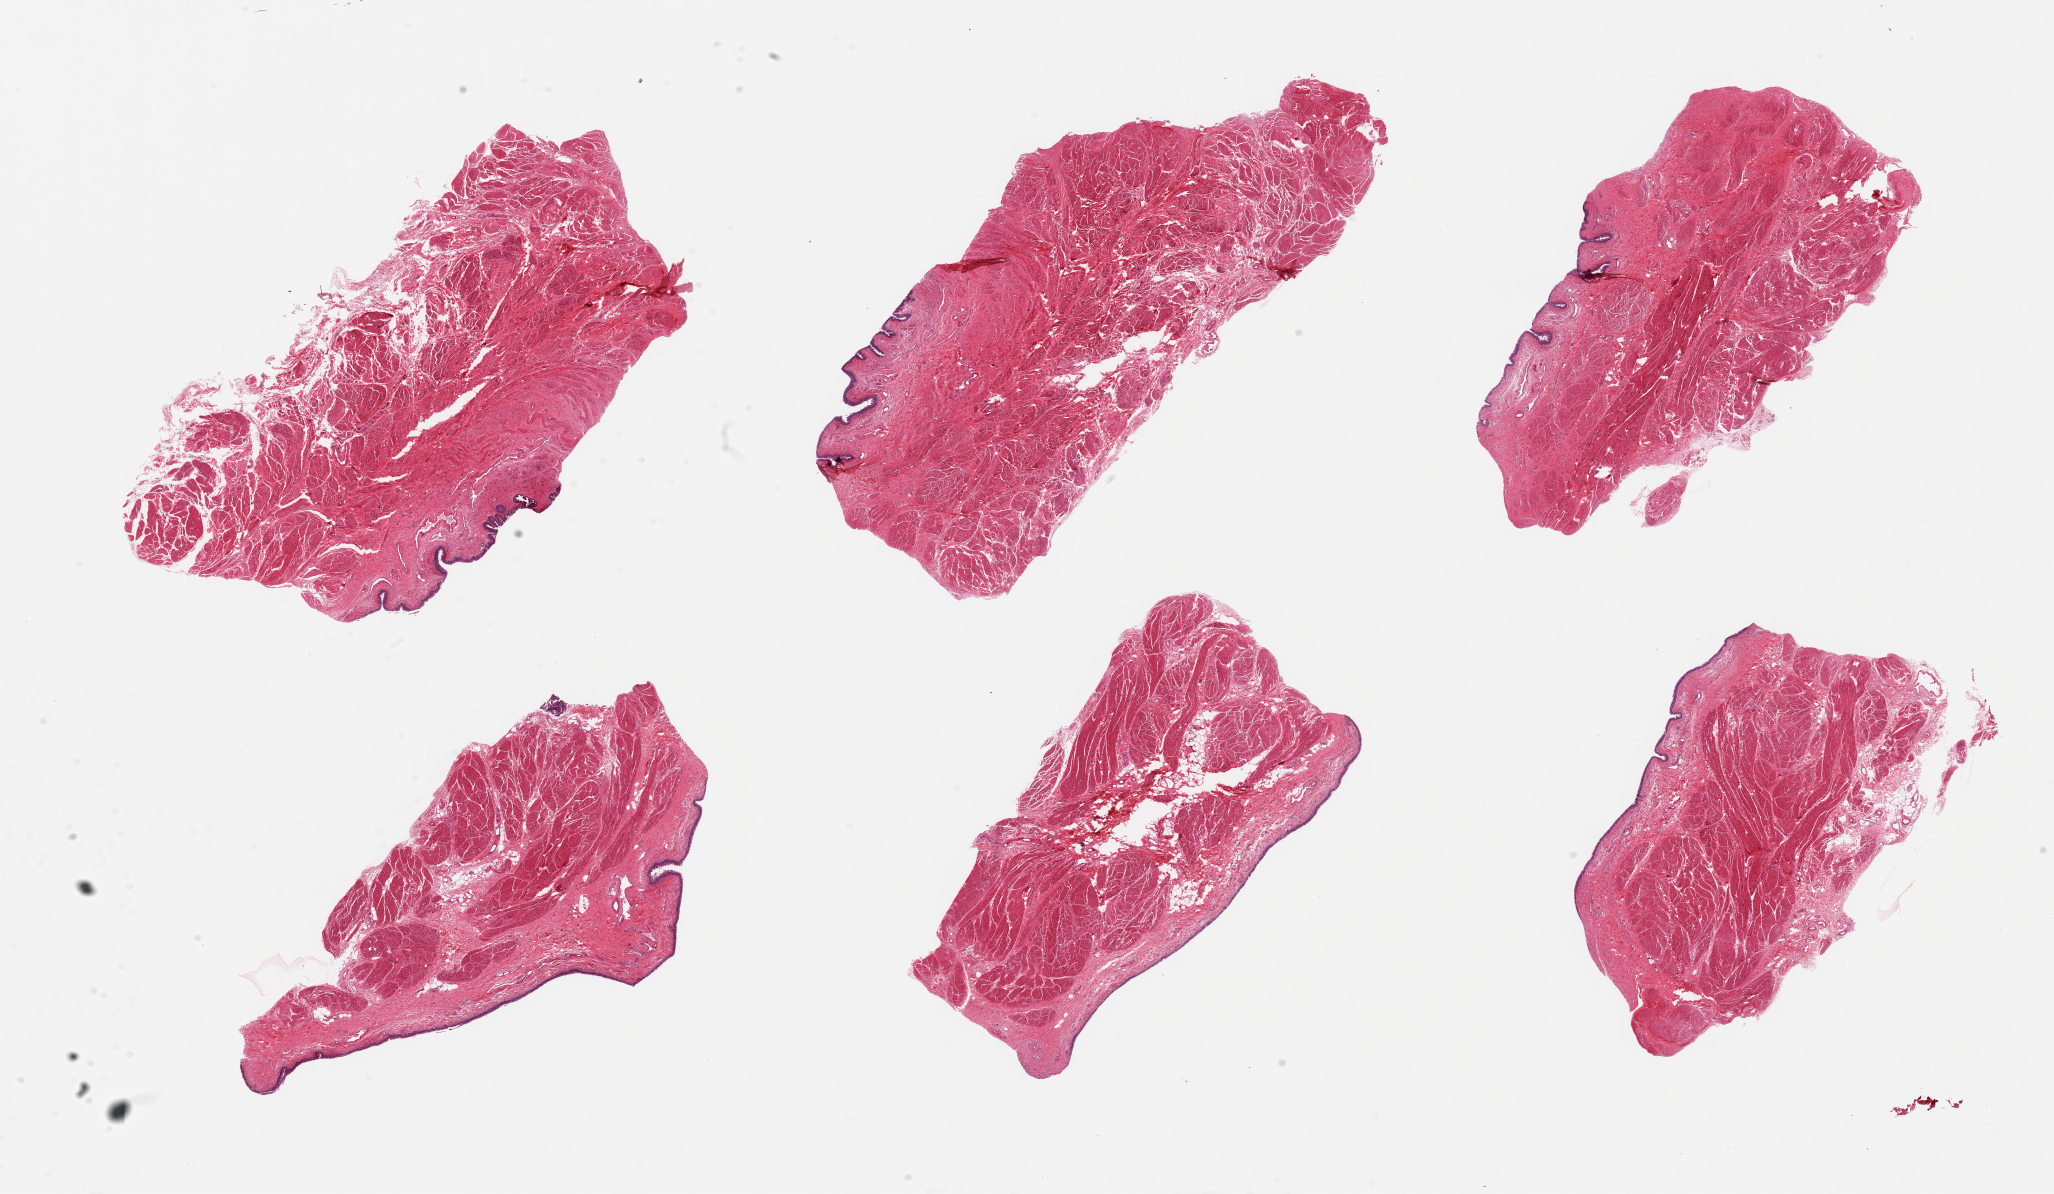
Digitized haematoxylin and eosin-stained section, brightfield, low-resolution overview of the scanned area, about 32.5 x 18.9 mm (slide scanned at 20x), PAXgene-fixed, paraffin-embedded tissue, target tissue: urinary bladder, tissue donor sample. Male donor.
Pathologist's review note for this sample: 6 pieces ~10x4mm. Urothelium variably sloughed, better preserved than usual, less than 1% of thickness.